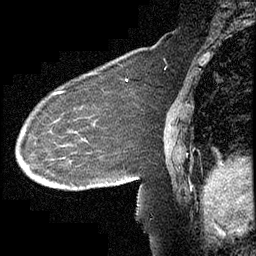
Breast MRI (dynamic contrast-enhanced), one sagittal slice; slice 149 of 232 in the series (ordered by position); dynamic contrast-enhanced study with each time point stored as its own series, time point 2 of 4 at this slice position (early post-contrast, ordered by acquisition time); 1.5 T; TE 4.2 ms, TR 6.7 ms; 3 mm slice thickness; 256 × 256 image matrix, field of view 200 × 200 mm. Female patient, age 63 years. Case-level facts recorded for this patient, not image findings: setting: breast cancer imaged before/during neoadjuvant chemotherapy; receptor status: triple-negative.
Annotated regions visible in this slice (semi-automatic segmentation, software-assisted and operator-edited):
- analysis volume of interest (the breast-tissue region the enhancement analysis was run in; not a lesion): bounding box <16,90,140,211> (left, top, right, bottom; pixels)
- tumour enhancement mask (voxels above the 70 % enhancement threshold inside the analysis volume of interest): <56,91,63,93>